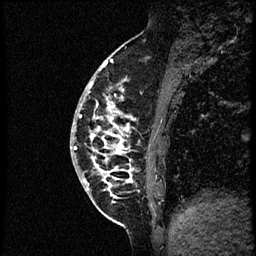
Breast MRI (dynamic contrast-enhanced), one sagittal slice. Position 18 of 56 along the scan axis. Dynamic contrast-enhanced study with each time point stored as its own series, time point 2 of 3 at this slice position (early post-contrast, ordered by acquisition time). 1.5 T. TE 4.2 ms, TR 21.3 ms. 256 × 256 image matrix. Patient: female, 41 years. Case-level facts recorded for this patient, not image findings: setting: breast cancer imaged before/during neoadjuvant chemotherapy; receptor status: HER2-positive.
Annotated regions visible in this slice (semi-automatic segmentation, software-assisted and operator-edited):
- analysis volume of interest (the breast-tissue region the enhancement analysis was run in; not a lesion): bounding box <70,73,175,205> (left, top, right, bottom; pixels)
- tumour enhancement mask (voxels above the 100 % enhancement threshold inside the analysis volume of interest): <73,81,133,194>